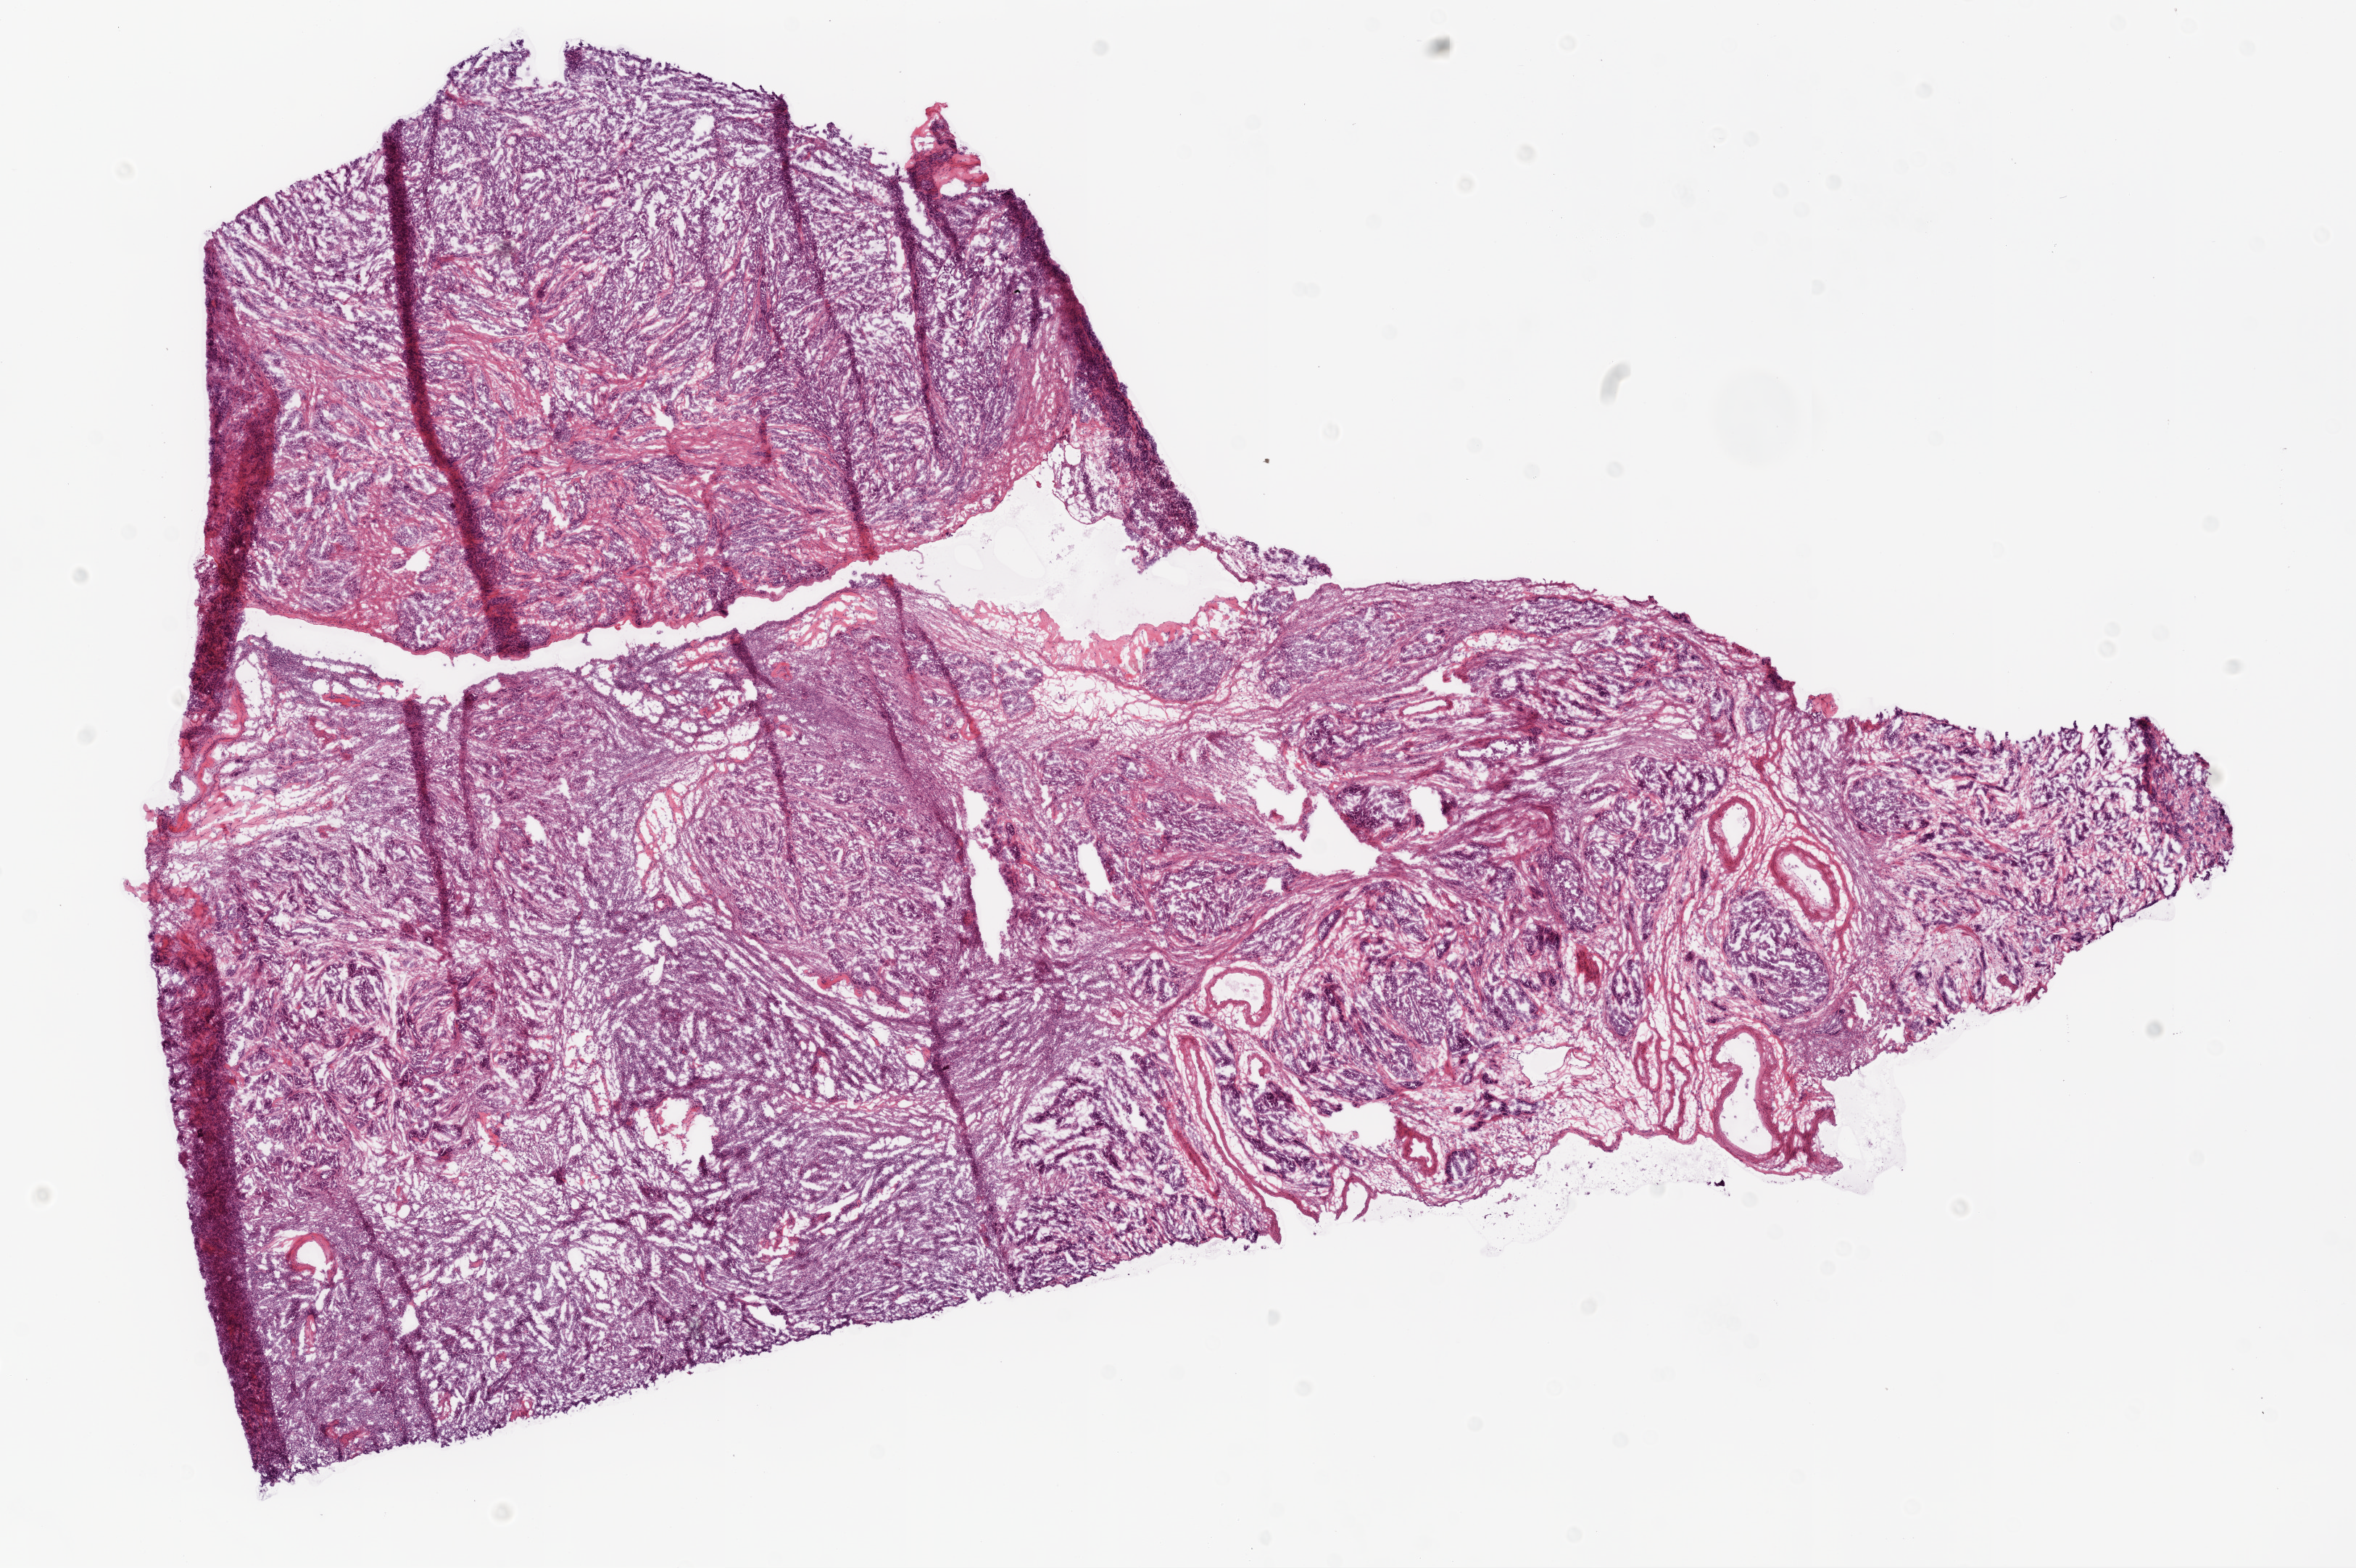
H&E whole-slide image — whole scanned area (about 13.0 x 8.7 mm) shown as a low-resolution overview; frozen section from the bottom of the tissue portion; sample: primary tumour, ovary. Female, age 51 years at initial diagnosis. Pathologist review of this section (percent, as recorded): tumour cells 90%, tumour nuclei 90%.
Pathologic diagnosis: Serous cystadenocarcinoma, NOS.